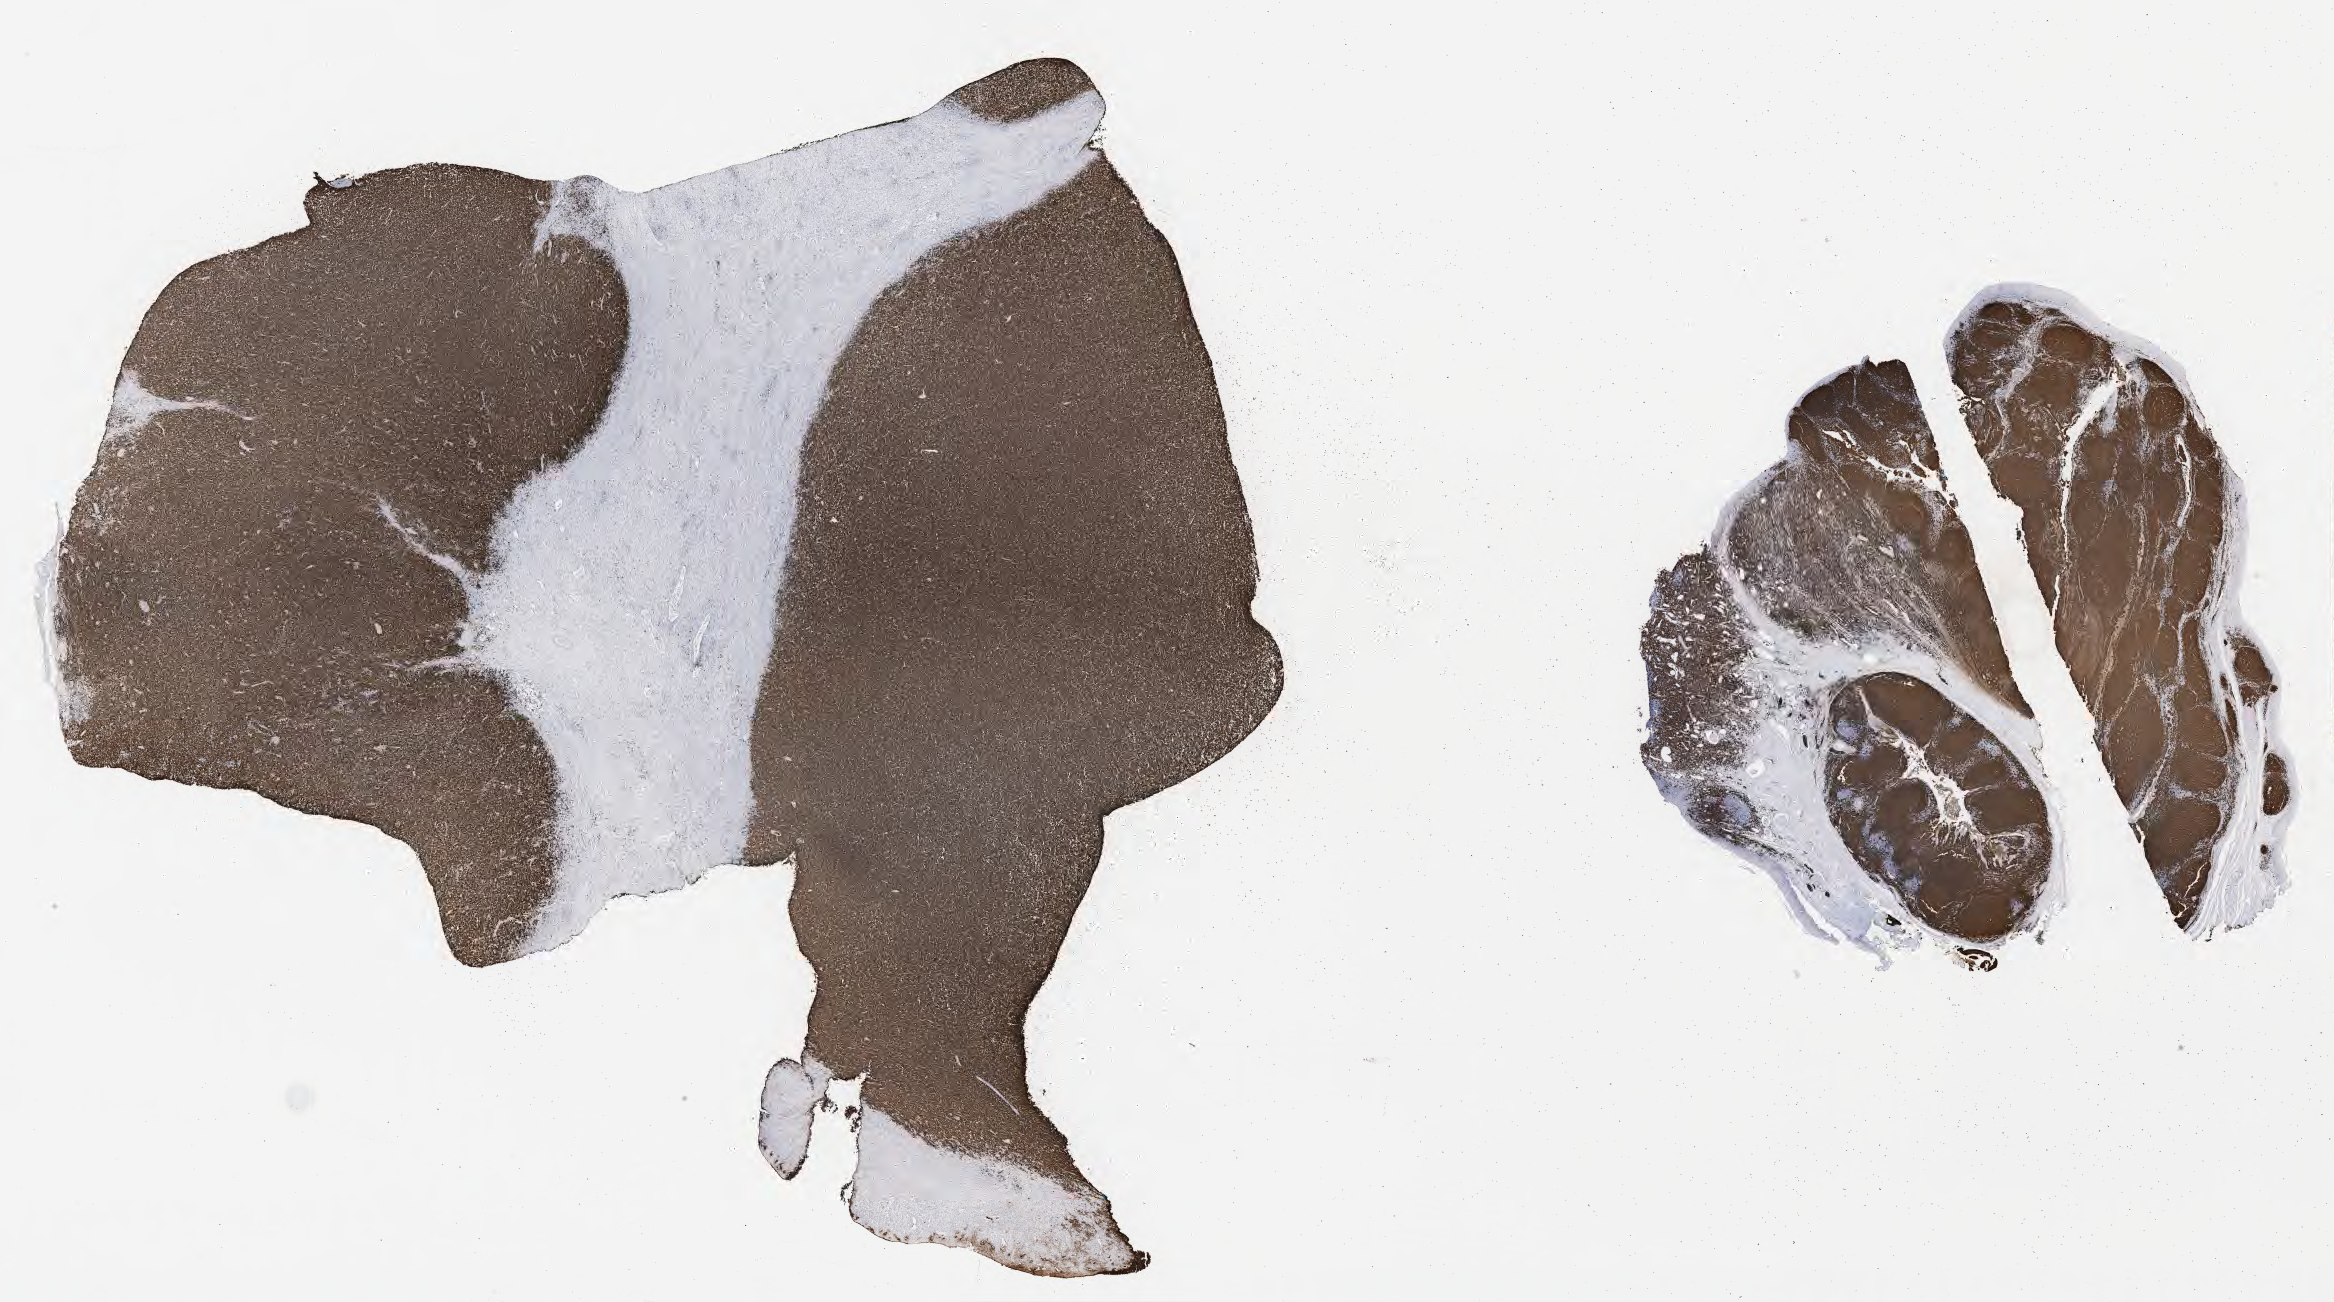
IHC for CD20, whole-slide image, low-resolution overview of the scanned area, about 37.7 x 21.0 mm; tumor tissue. Female, age 8 years at initial diagnosis.
Histologic diagnosis: Burkitt lymphoma, NOS.